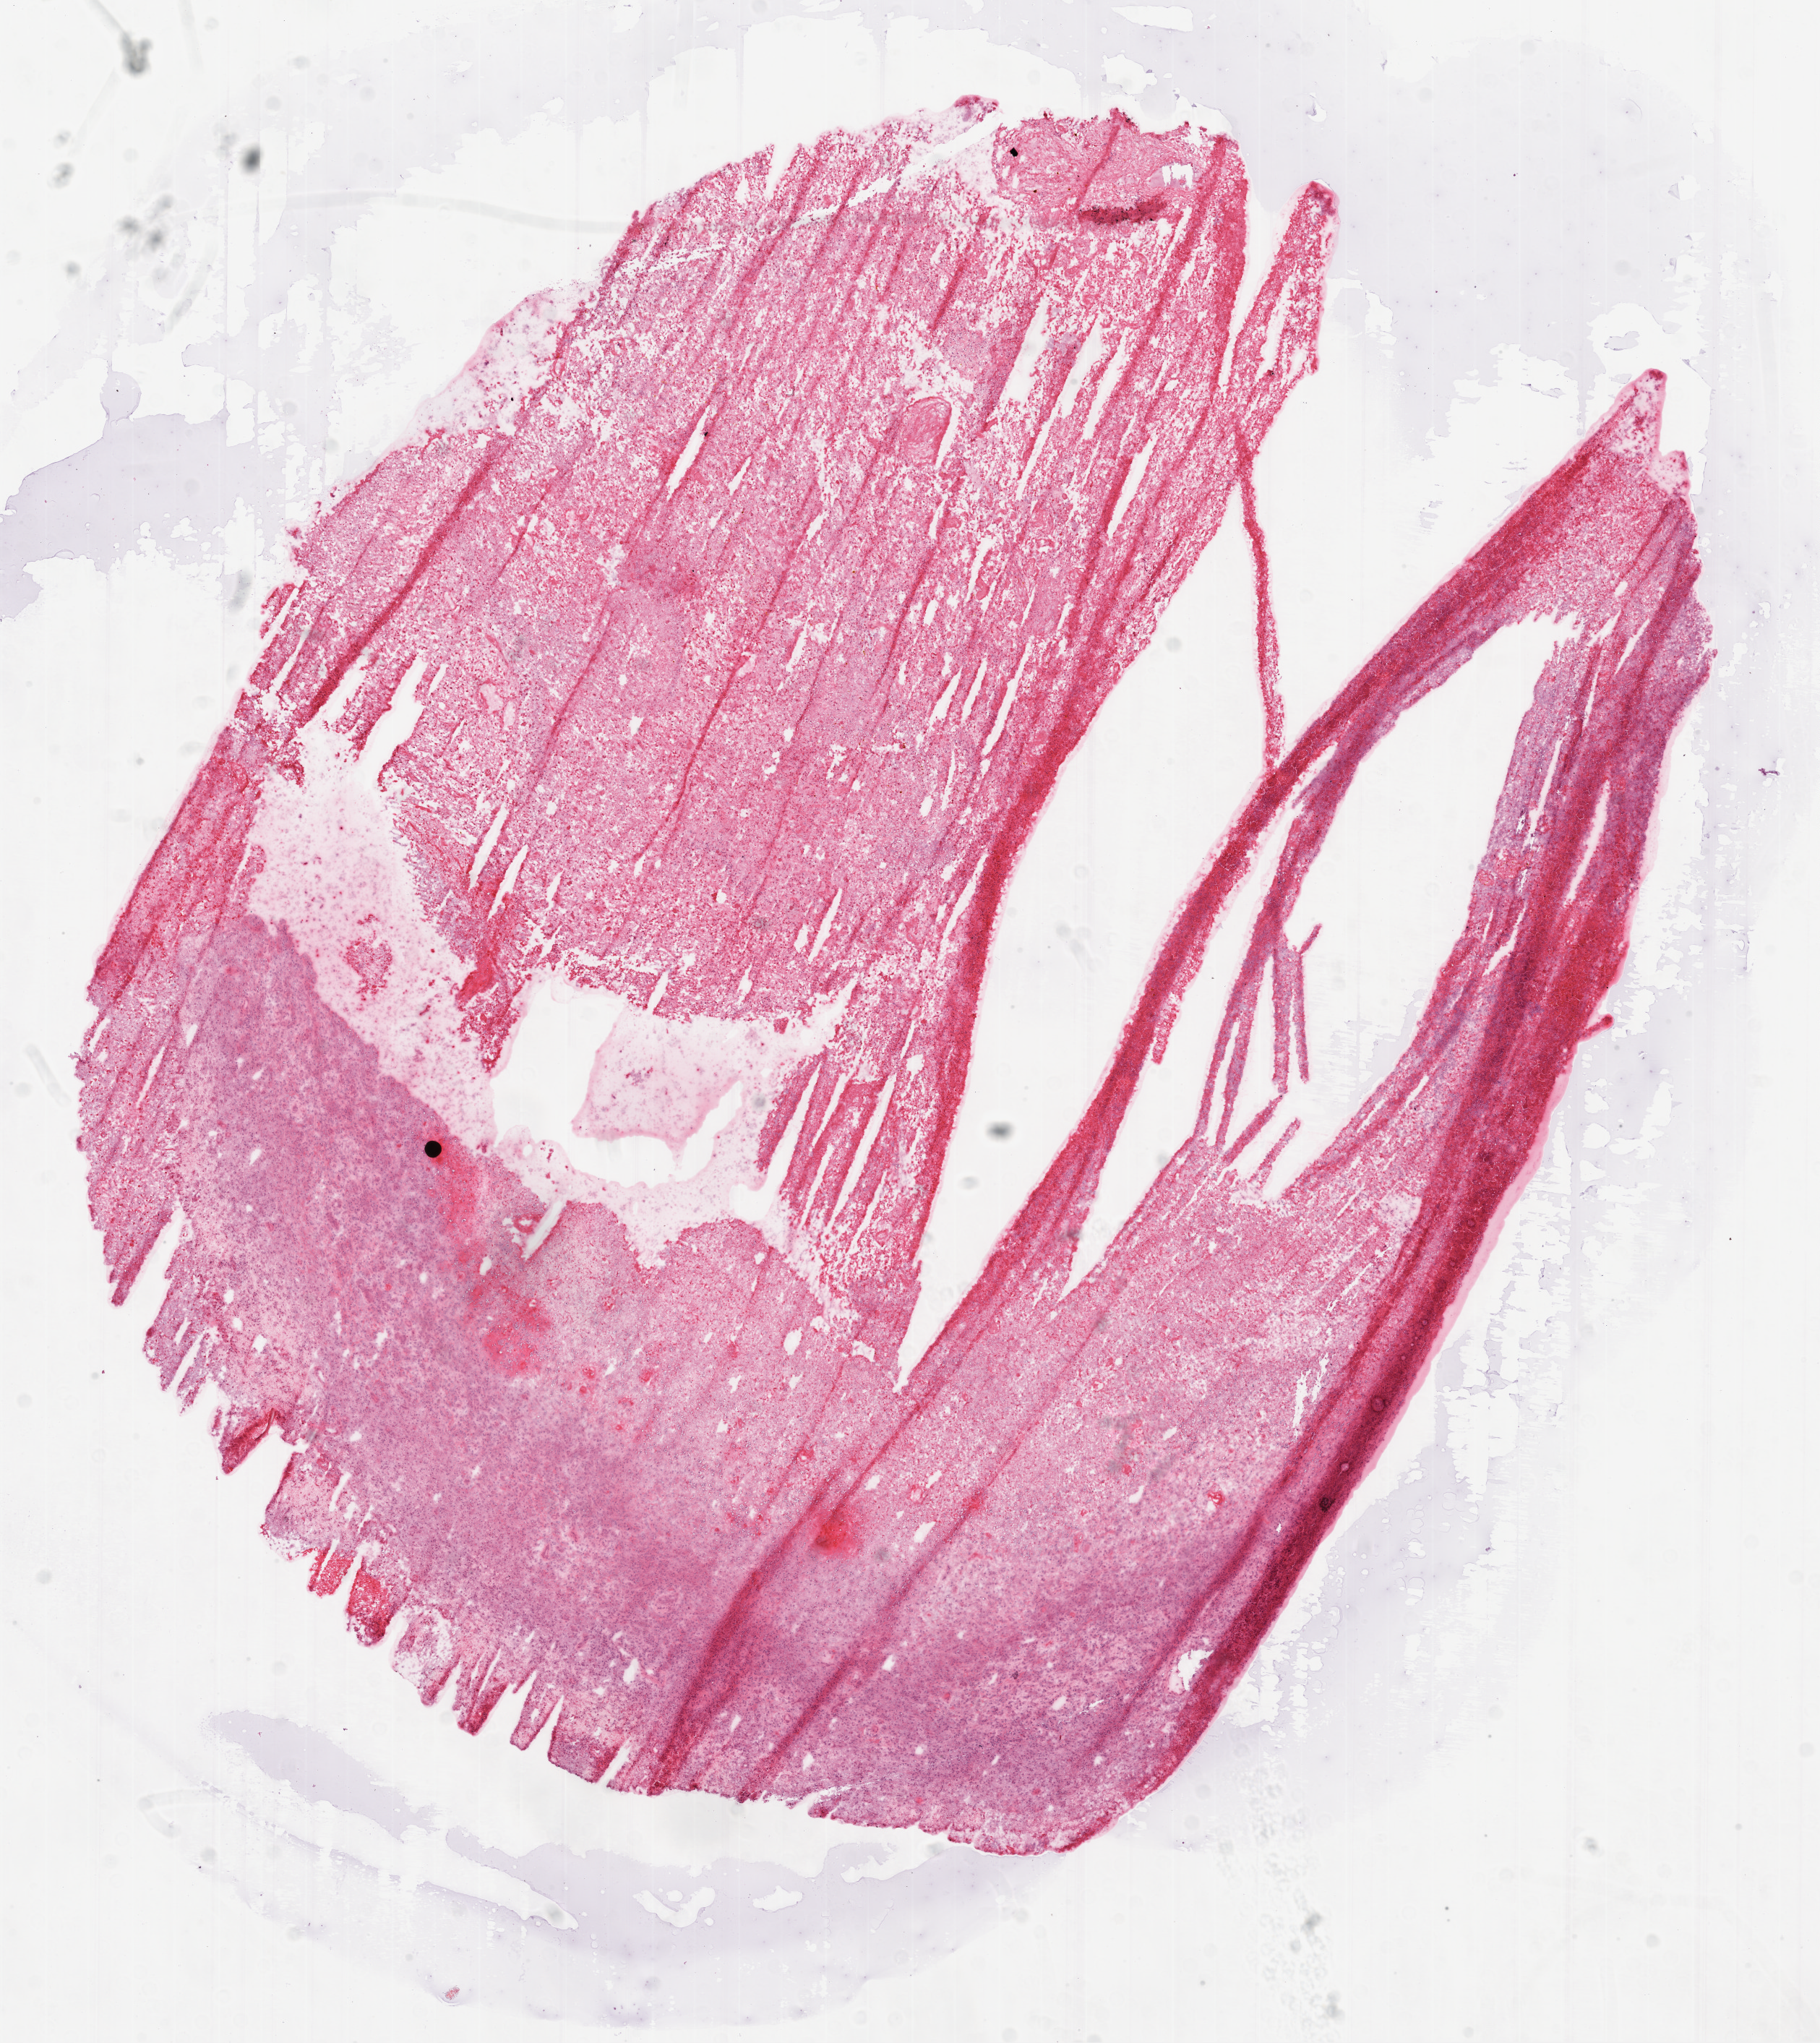
Hematoxylin and eosin (H&E) stained whole-slide image — shown as a low-resolution overview of the whole scanned area (about 10.2 x 11.4 mm, slide scanned at 20x). Frozen section from the bottom of the tissue portion. Brain, primary tumour sample. Male patient; age at initial diagnosis 40 years. Composition of this section per pathologist review: tumour nuclei 0%, necrosis 0%.
Histologic diagnosis: Glioblastoma.